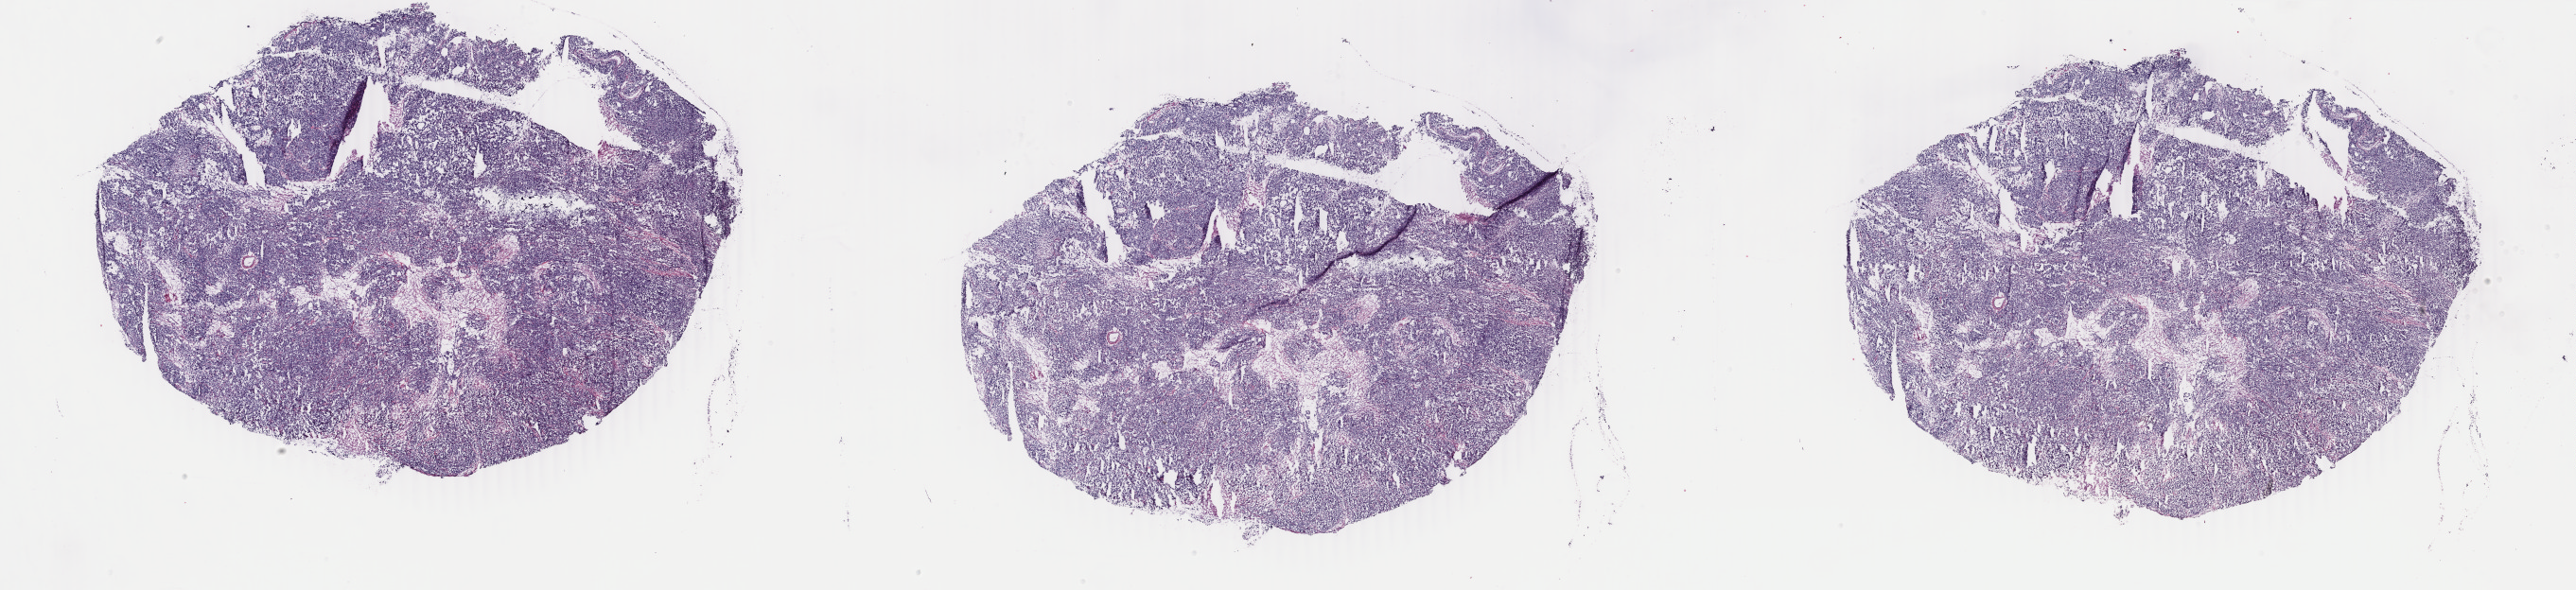
Whole-slide histology image, H&E — low-resolution overview of the scanned area, about 43.3 x 9.9 mm (acquisition: 40x scan), frozen section, primary tumour sample from the uterus. Patient: female, age at initial diagnosis 61 years. Histologic grade: G3 (poorly differentiated). Pathologist review of this section (percent, as recorded): tumour cells 95%, tumour nuclei 90%, normal cells 0%, stromal cells 0%, necrosis 5%. Inflammatory infiltration, as recorded: lymphocyte infiltration 0%, monocyte infiltration 0%, neutrophil infiltration 0%.
Diagnosis: Serous cystadenocarcinoma, NOS (endometrium). FIGO stage: IIIC2.